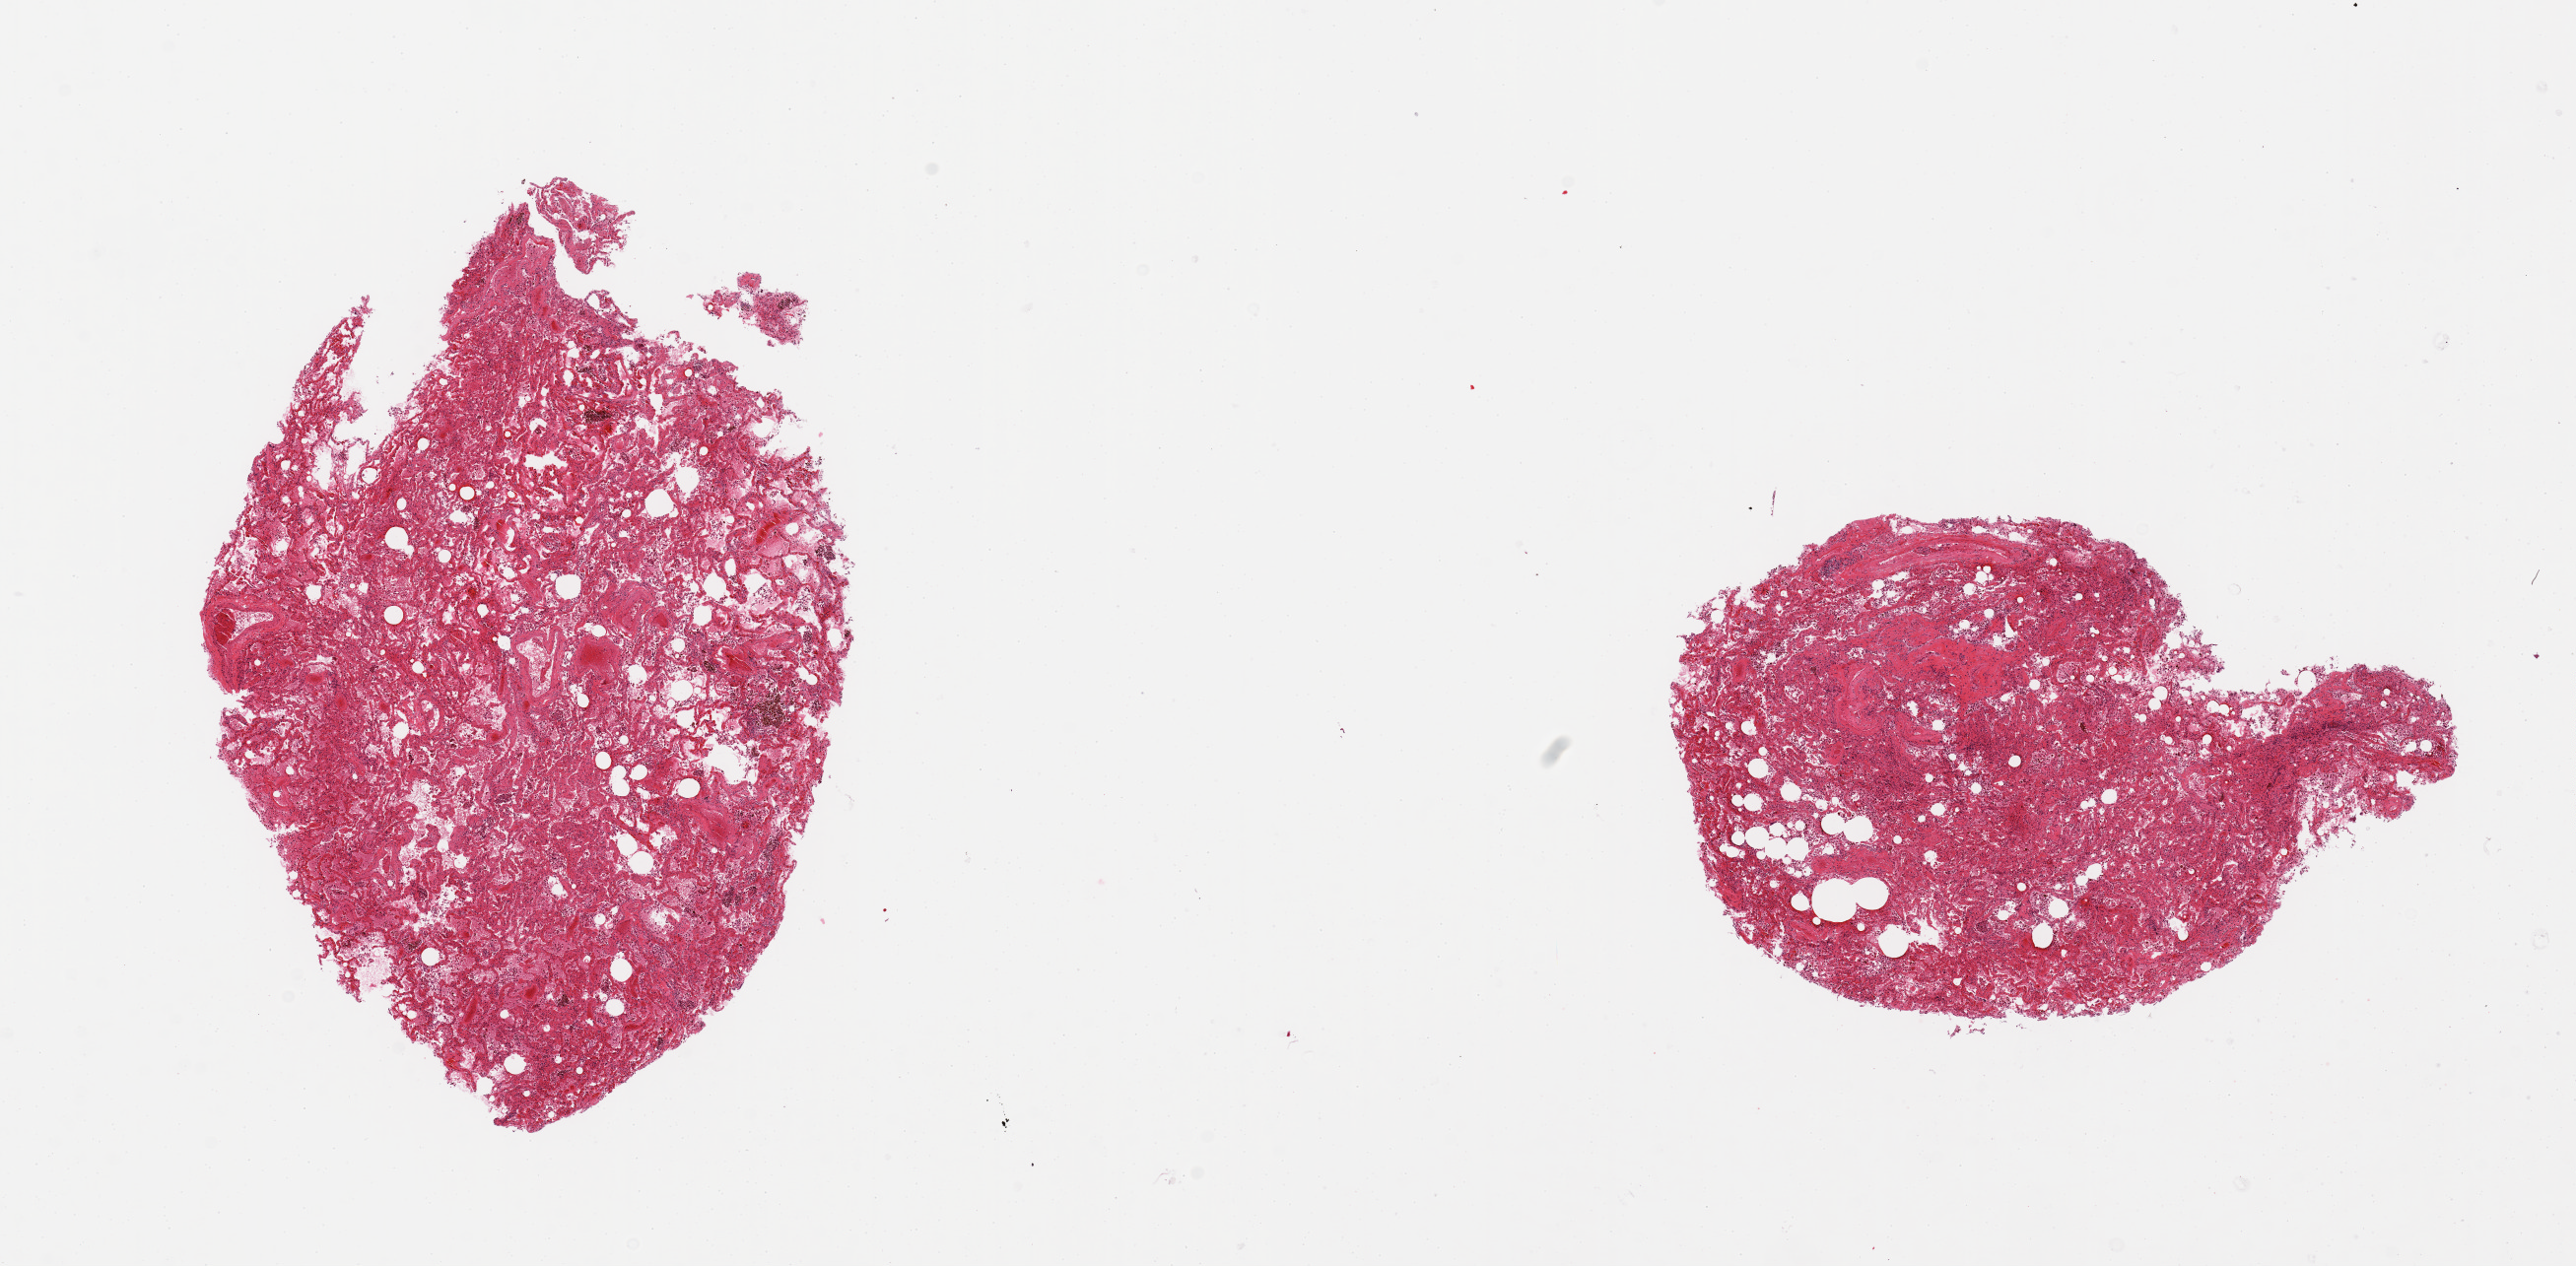
Haematoxylin and eosin whole-slide image — whole scanned area (about 20.7 x 10.2 mm) shown as a low-resolution overview, PAXgene-fixed paraffin-embedded (PFPE) section, sampled site (target tissue): lung, donor tissue sample. Female donor.
Review note (as recorded): 2 pieces, moderate congestion/moderate to marked autolysis.